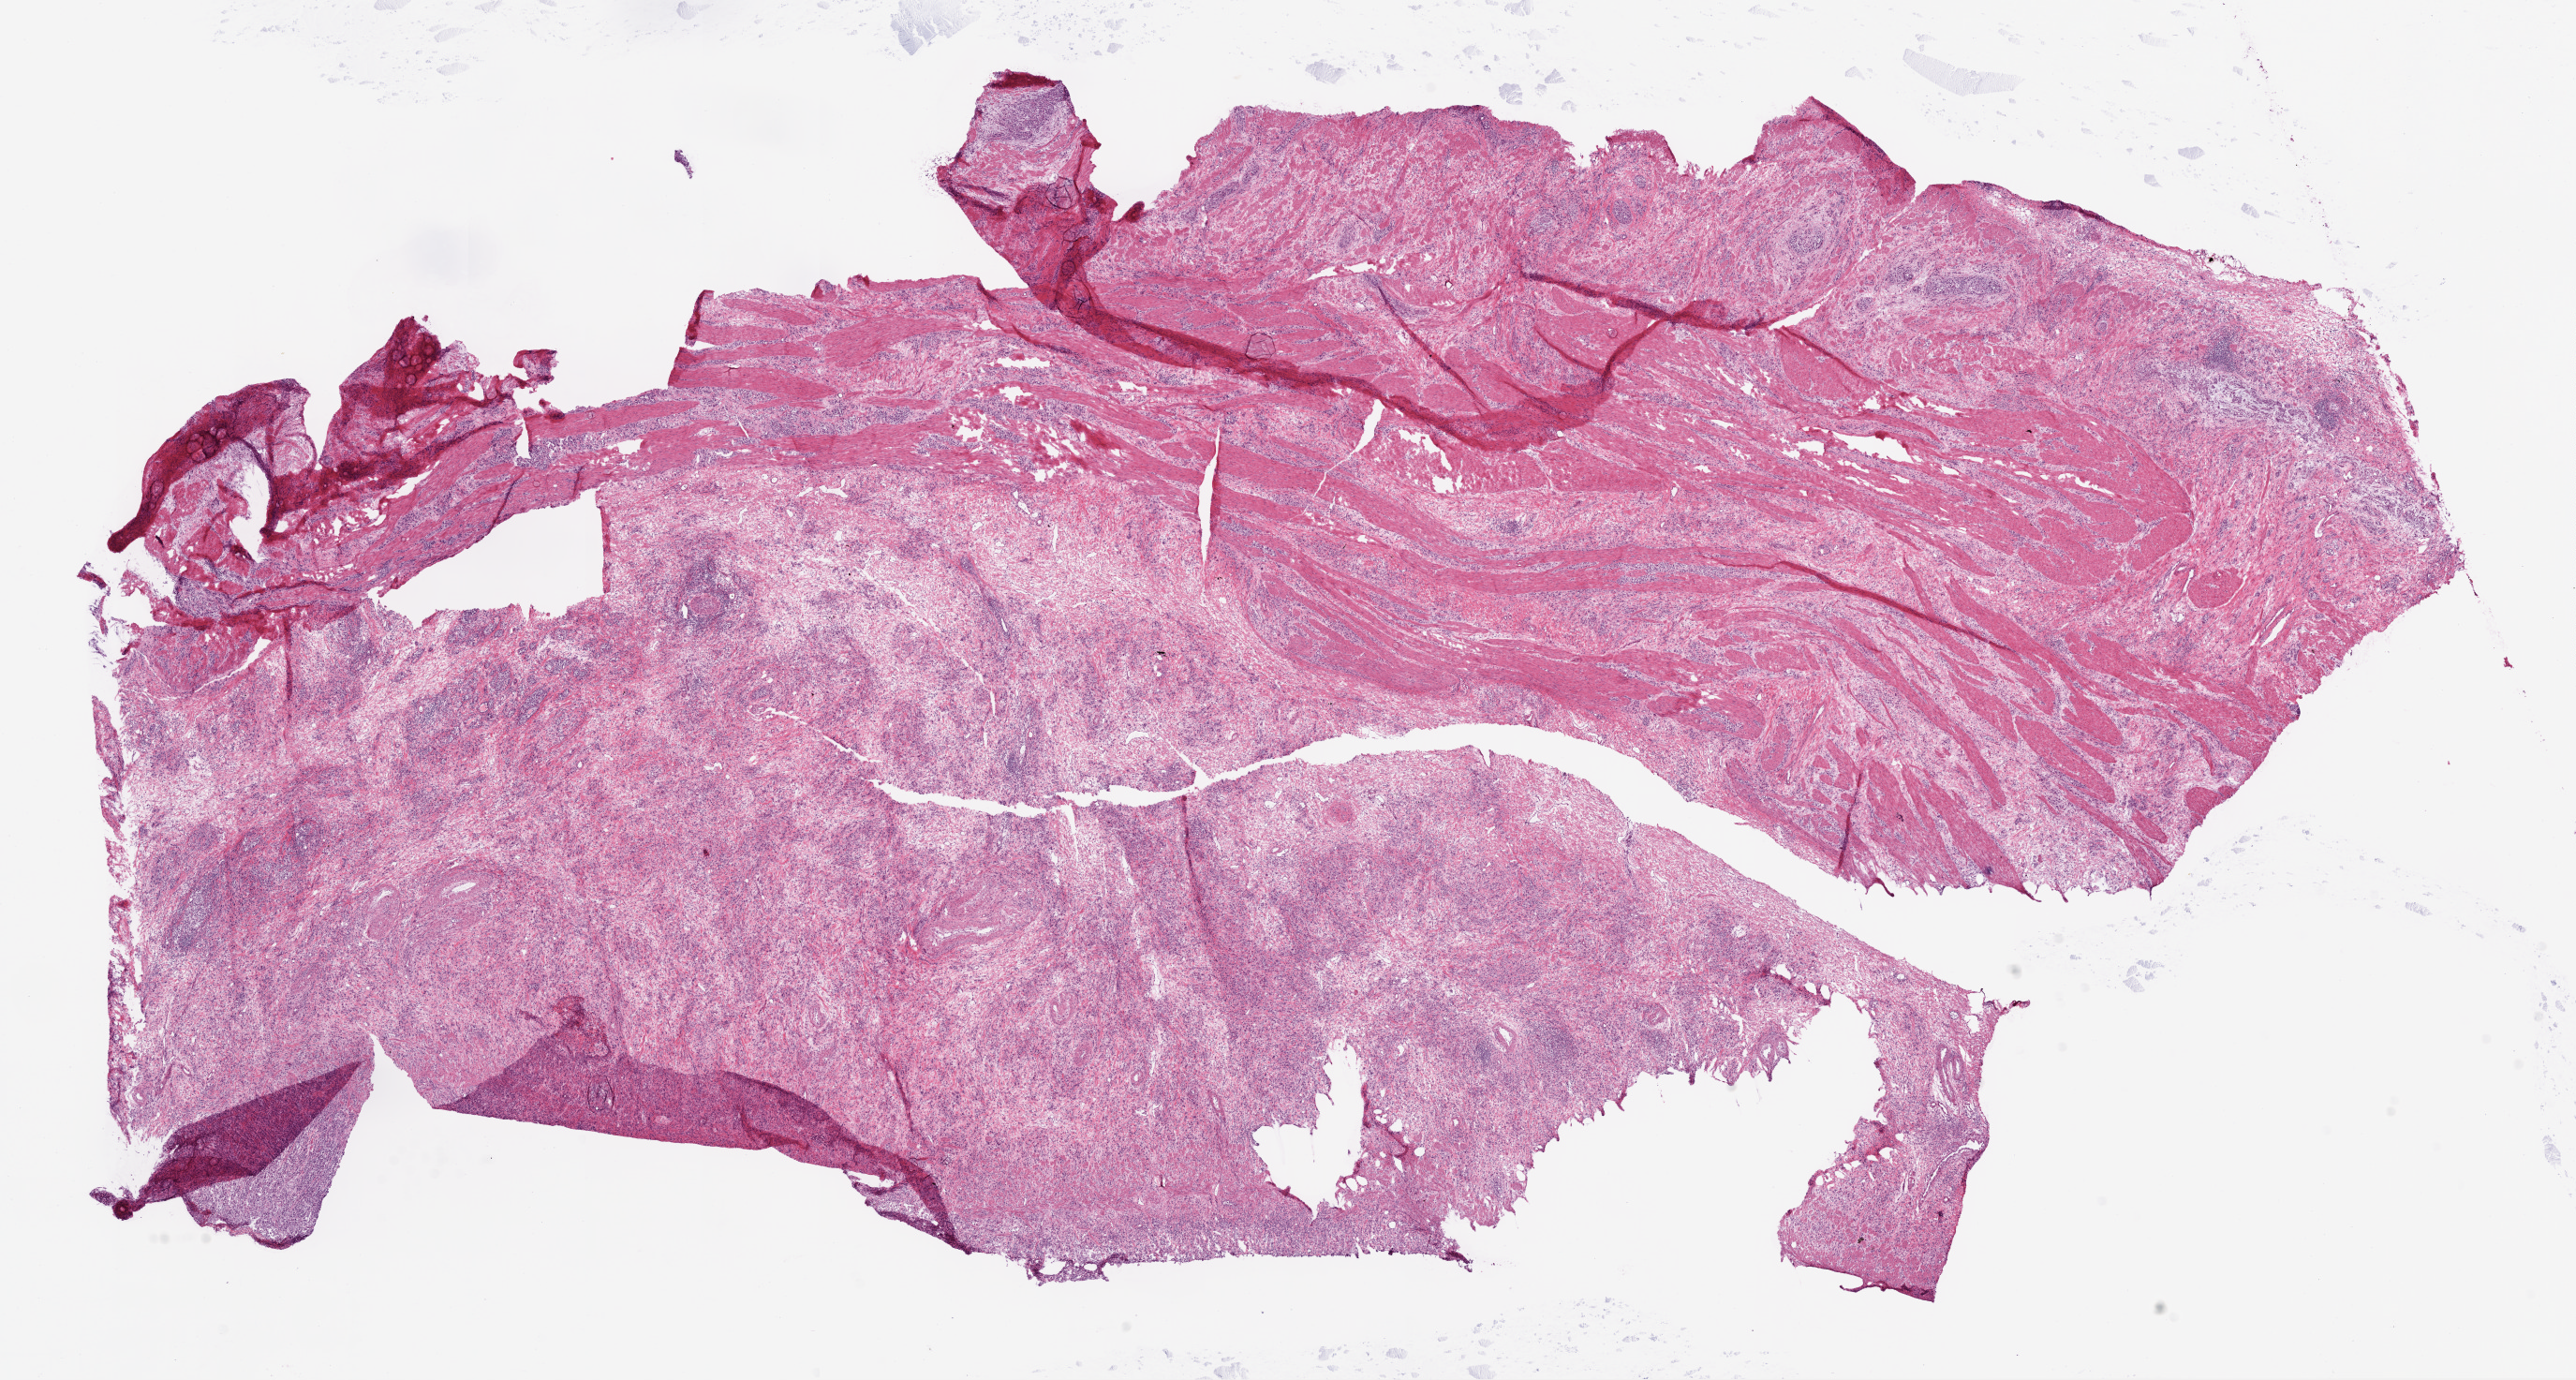
H&E whole-slide image — whole scanned area (about 22.1 x 11.8 mm) shown as a low-resolution overview. Frozen section from the bottom of the tissue portion. Primary tumour sample from the stomach. Female patient; age at initial diagnosis 76 years. Histologic grade: G3 (poorly differentiated). Slide review estimates, as recorded: tumour cells 79%, tumour nuclei 75%, normal cells 1%, stromal cells 20%, necrosis 0%.
- diagnosis: Adenocarcinoma, NOS
- AJCC pathologic stage: IIIA